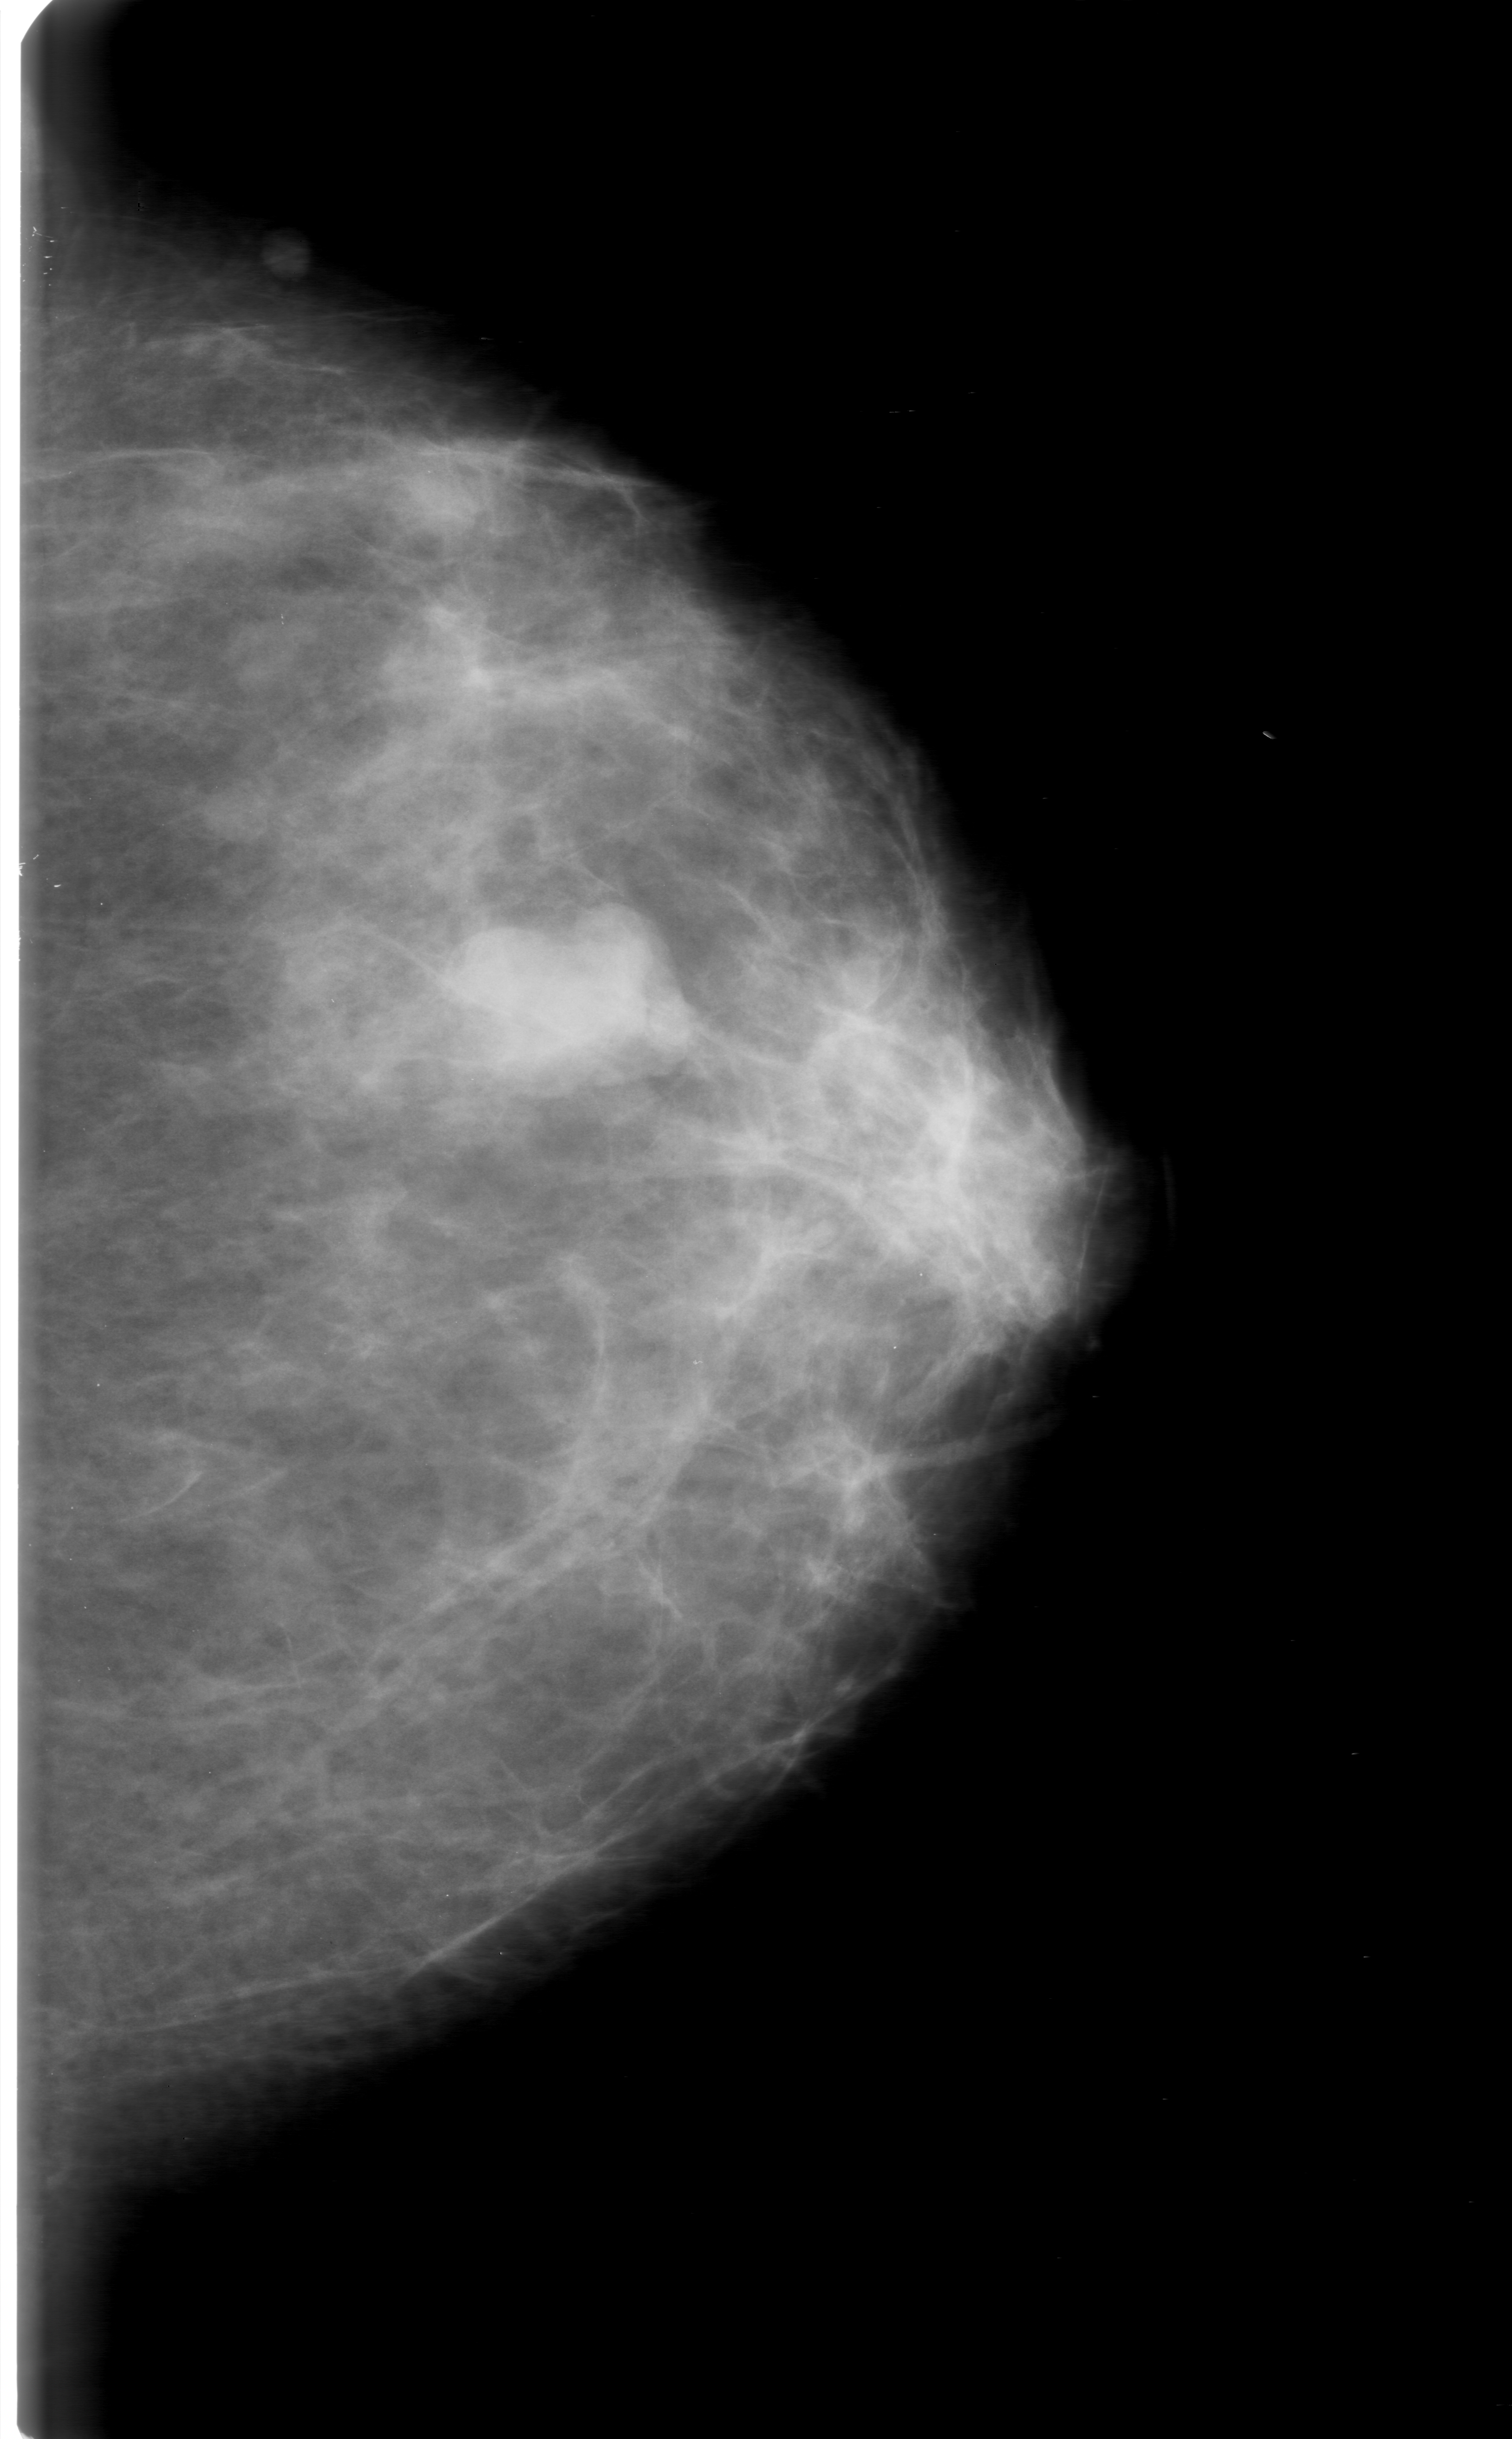
Mammogram (digitized film); left breast; CC view; BI-RADS breast density category 3 (scale 1–4); 1512 × 2439 image matrix.
Marked abnormalities (boxes around the expert regions of interest):
- mass, shape lobulated, margins circumscribed; BI-RADS assessment category 0 (incomplete: needs additional imaging); pathology result (as recorded, not read from the image): benign: bounding box [x1, y1, x2, y2] px = [456, 906, 657, 1084]